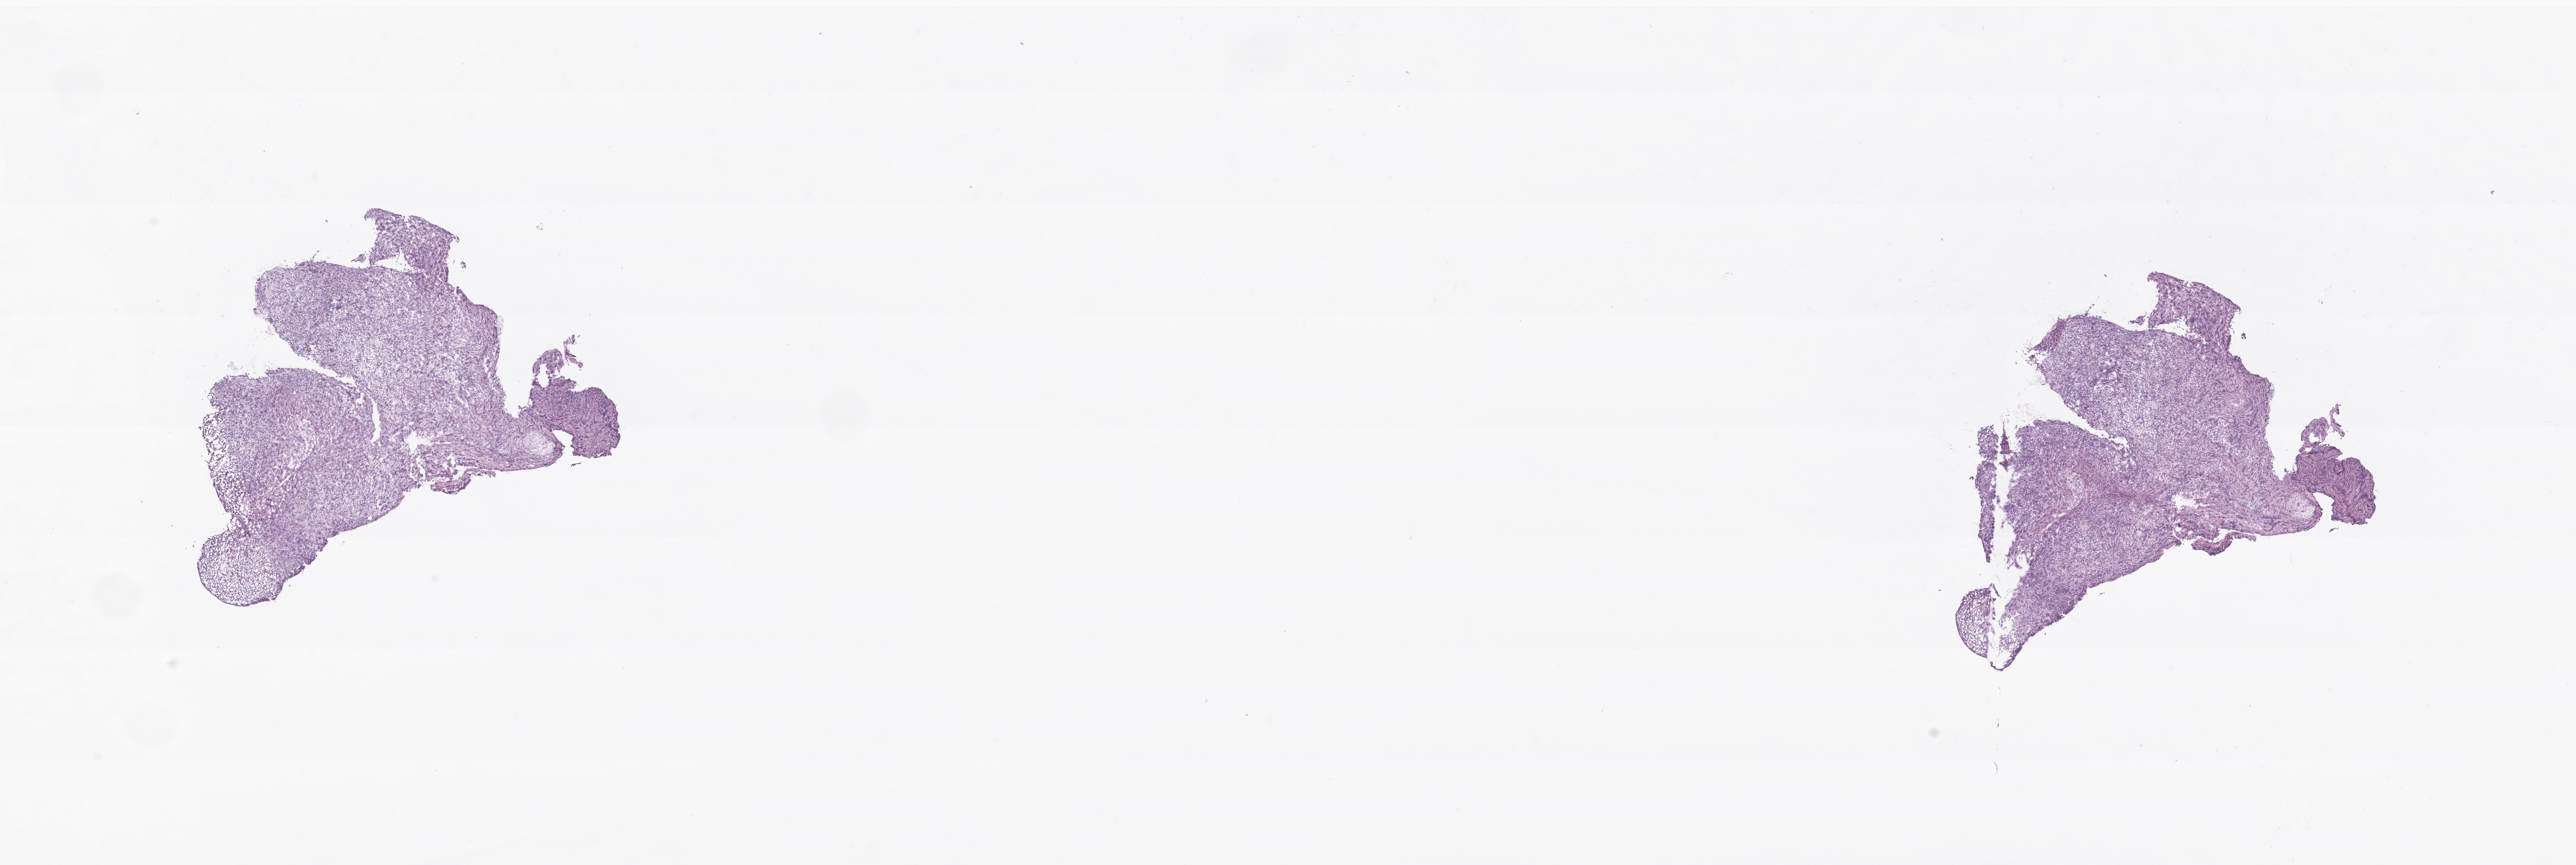
Digitized hematoxylin and eosin (H&E)-stained section of tumor tissue from the brain stem, whole scanned area (about 24.6 x 8.3 mm) shown as a low-resolution overview, frozen section. Patient: male, age 149 months (12 years 5 months).
- diagnosis (ICD-O-3 morphology term): Medulloblastoma, NOS